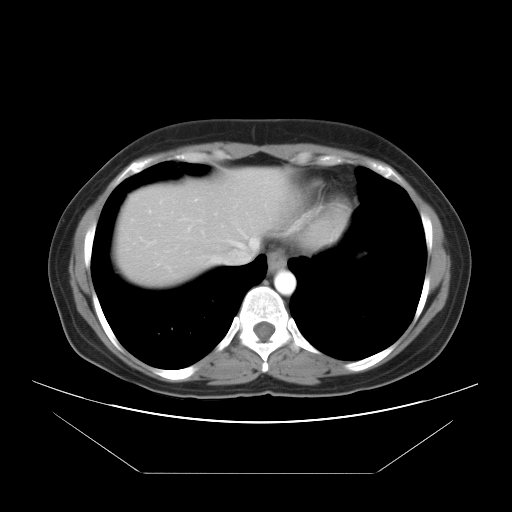
Contrast-enhanced abdominal CT, one axial slice. Position 32 of 34 along the scan axis. 120 kVp. Intravenous contrast given. Soft-tissue window (W 400 / L 40 HU). 512 × 512 image matrix, field of view 410 × 410 mm. Female patient, age 38 years. Case-level facts recorded for this patient, not image findings: diagnosis: colorectal cancer liver metastases, imaged before liver resection; multiple liver metastases: yes; largest metastasis: 3.1 cm; chemotherapy before resection: no.
Structures marked on this image (manually delineated by an expert):
- hepatic veins: bounding box <178,218,257,263> (left, top, right, bottom; pixels)
- liver: <112,170,305,288>
- planned liver remnant (the part of the liver to remain after resection): <204,170,307,256>